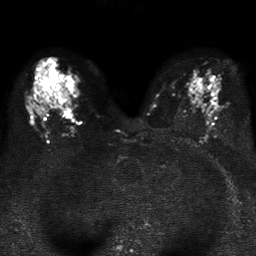
Breast MRI, one axial slice. Position 21 of 37 along the scan axis. Diffusion-weighted series; image 2 of 4 stored at this slice position (different b-values; order by instance number). 1.5 T. 5 mm slice thickness. 256 × 256 image matrix, field of view 320 × 320 mm. Female patient.
Structures marked on this image (outlined manually by an expert reader):
- tumour on diffusion-weighted imaging: box from (x=59, y=90) to (x=67, y=104) px